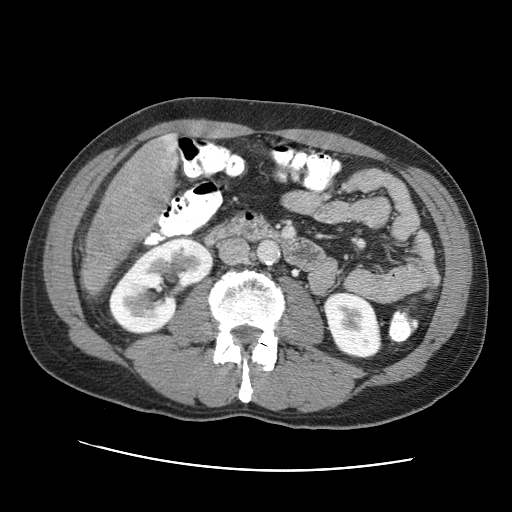
Contrast-enhanced abdominal CT (liver protocol), one axial slice; slice 15 of 95 in the series (ordered by position); one of 2 acquisitions stored at this slice position; soft-tissue window (W 400 / L 40 HU); 2.5 mm slice thickness; 512 × 512 image matrix, field of view 360 × 360 mm. Case-level facts recorded for this patient, not image findings: diagnosis: hepatocellular carcinoma (patient treated with transarterial chemoembolisation; whether this scan precedes or follows treatment is not stated here); TNM stage (as recorded): Stage-IVA; Child-Pugh class: A; tumour differentiation: moderately differentiated; tumour nodularity: multinodular.
Outlined on this slice (semi-automatic segmentation, software-assisted and operator-edited):
- liver parenchyma outside the tumour (the mass and vessels are separate outlines, so this box may not span the whole liver): bounding box (x1, y1, x2, y2) in pixels: (84, 134, 178, 285)
- mass: (80, 135, 175, 293)
- liver vessels: (169, 134, 177, 161)